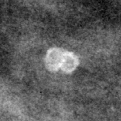
Region of interest cut from a scanned film mammogram (one marked finding), left breast, MLO view, BI-RADS breast density category 3 (scale 1–4).
Finding: calcifications, morphology round and regular / lucent centered; BI-RADS assessment category 2; subtlety rating 3 on a 1 (subtle) to 5 (obvious) scale; benign; no additional work-up was recommended (benign without callback).